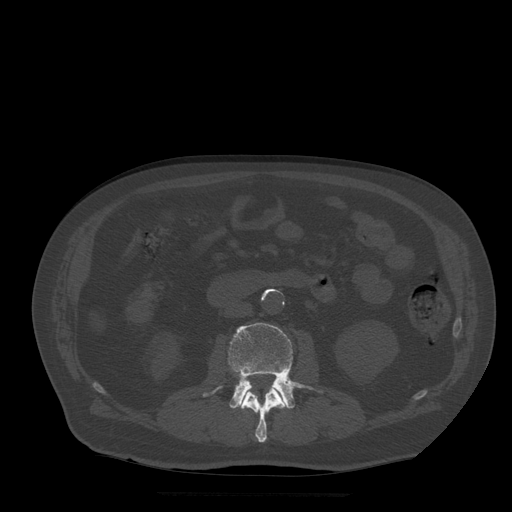
CT including the spine, one axial slice; slice 153 of 522 in the series (ordered by position); bone window (W 1800 / L 400 HU); 1.25 mm slice thickness; 512 × 512 image matrix, field of view 420 × 420 mm. Patient age 72 years. Case-level facts recorded for this patient, not image findings: primary cancer: prostate.
Structures marked on this image (semi-automatic segmentation, software-assisted and operator-edited):
- L2 vertebra: bounding box [x1, y1, x2, y2] px = [241, 387, 286, 443]
- L3 vertebra: [204, 323, 323, 409]